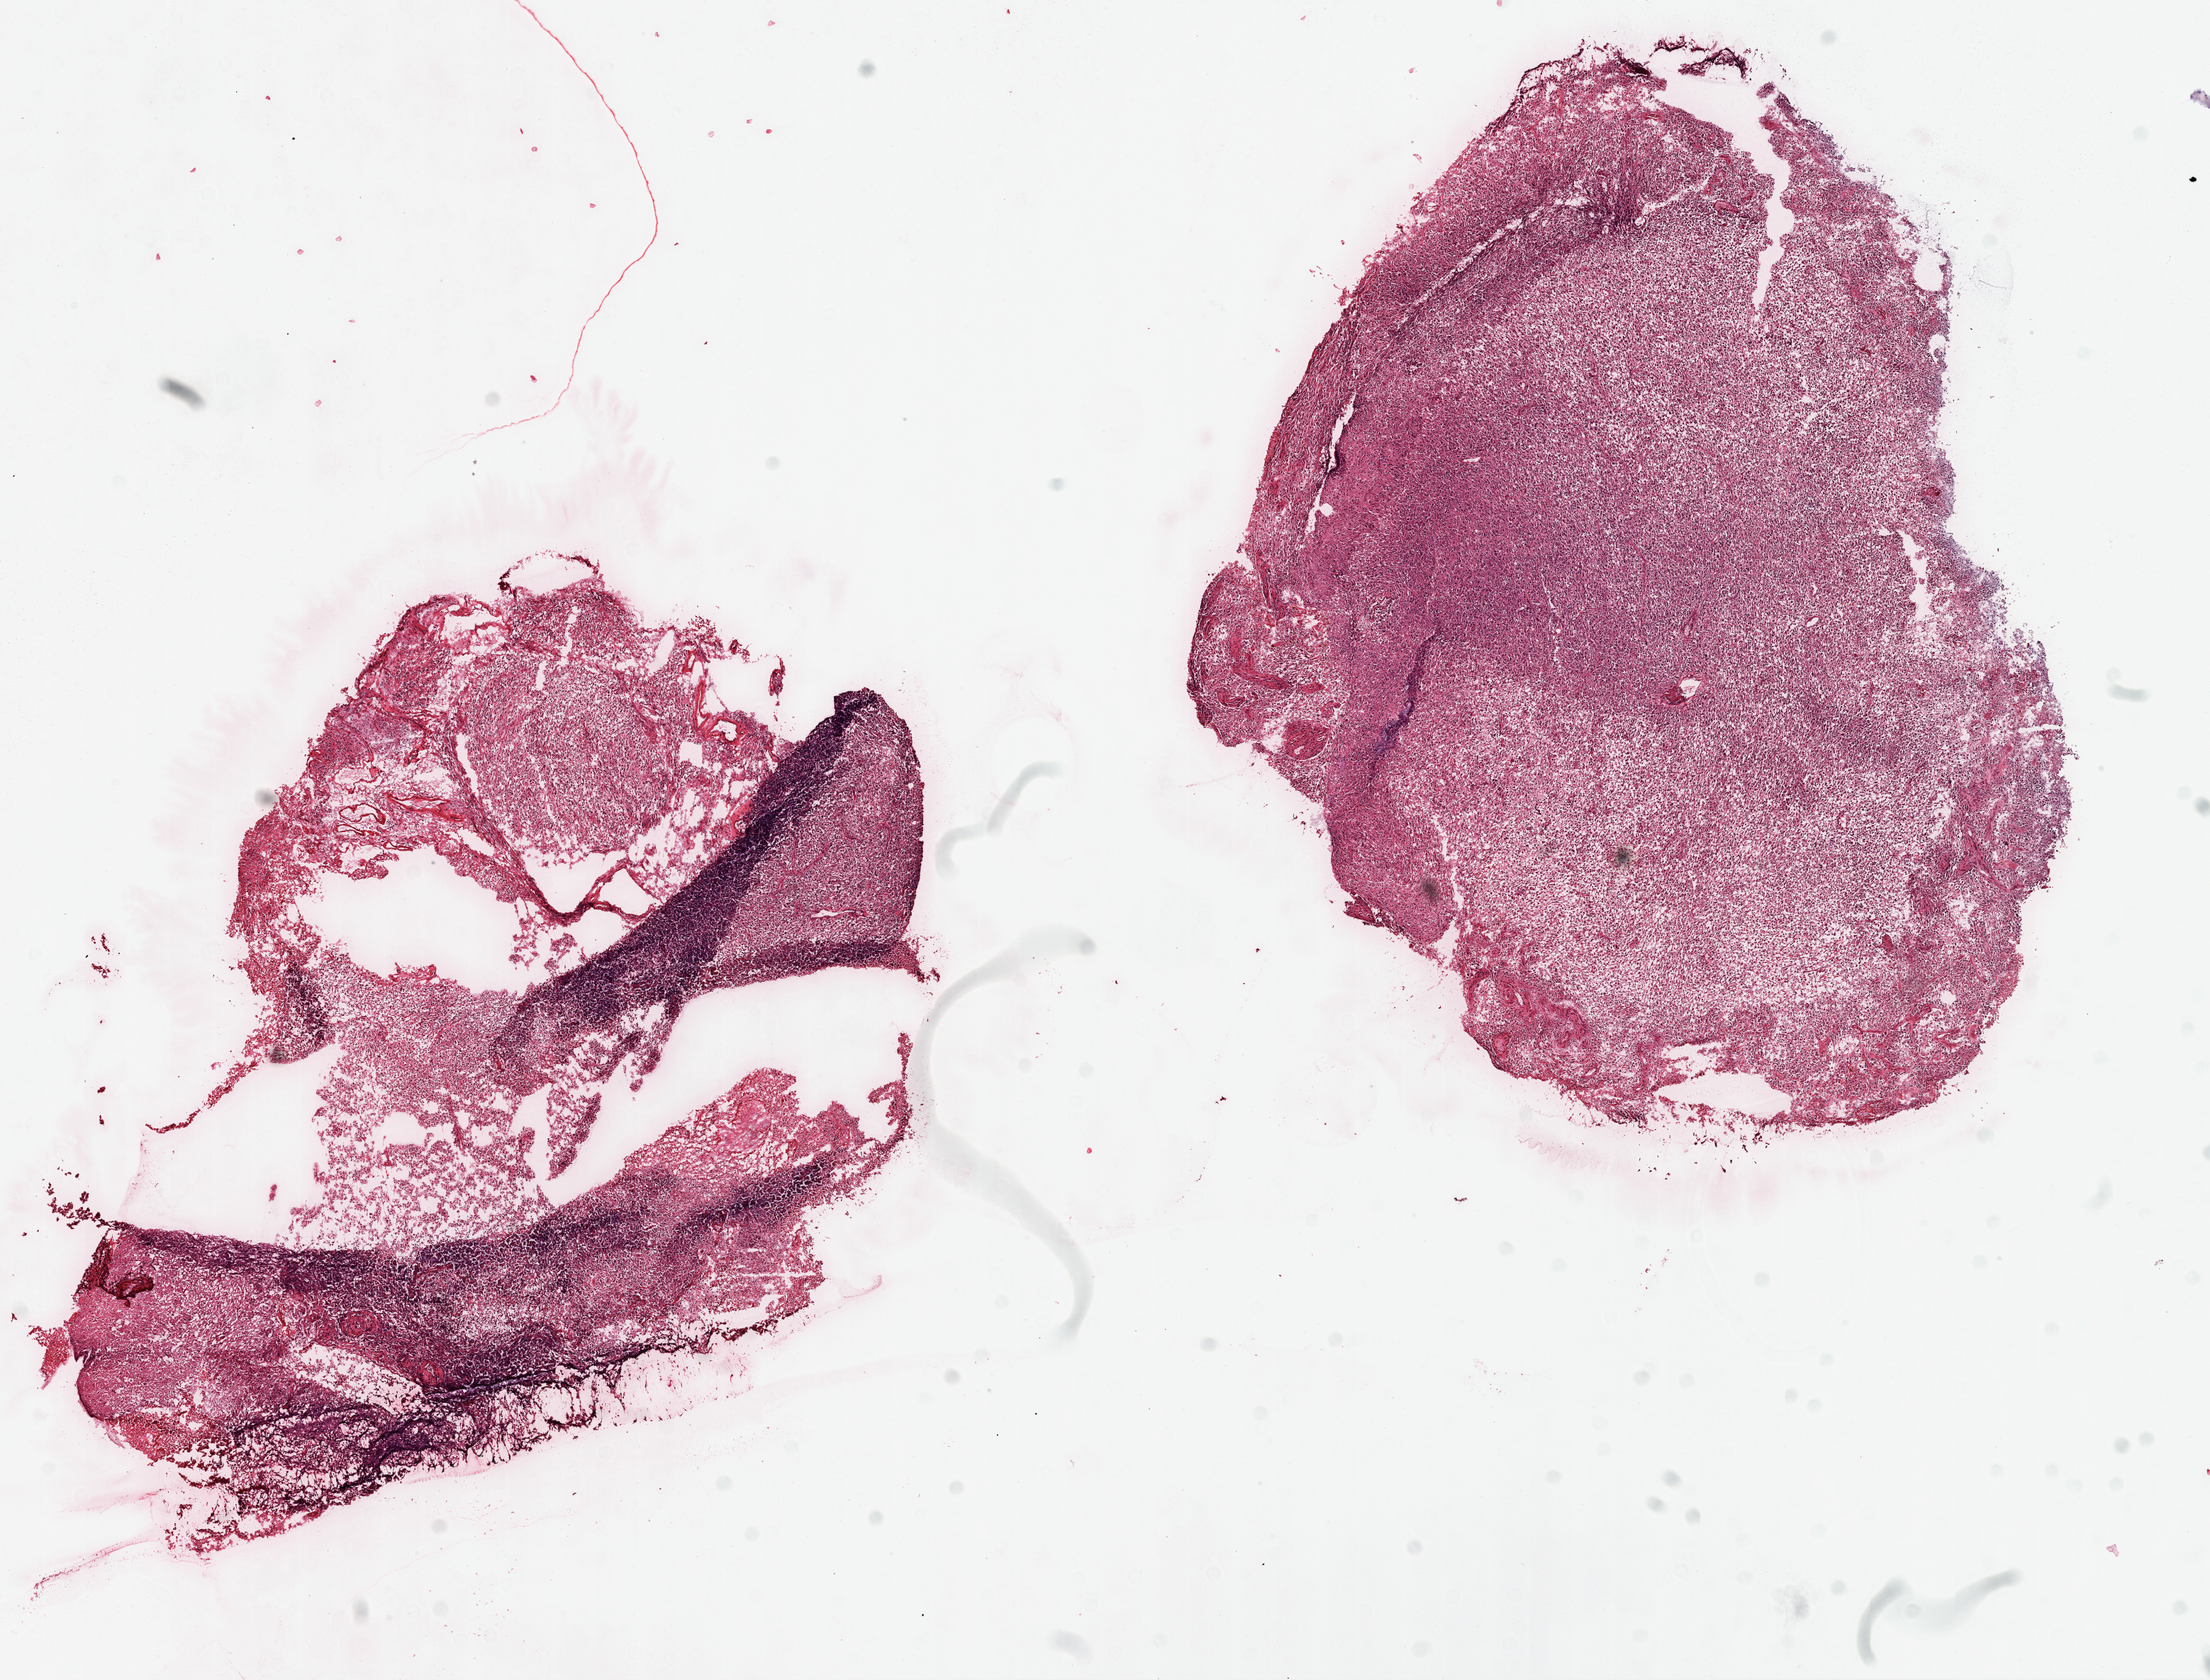
Digitized H&E-stained tissue section (whole slide), low-resolution overview of the scanned area, about 12.6 x 9.6 mm (slide scanned at 20x). Frozen section from the top of the tissue portion. Primary tumour sample from the brain. Male patient; age at initial diagnosis 69 years. Slide review estimates, as recorded: tumour cells 85%, tumour nuclei 95%, normal cells 0%, stromal cells 5%, necrosis 10%.
- pathologic diagnosis: Glioblastoma